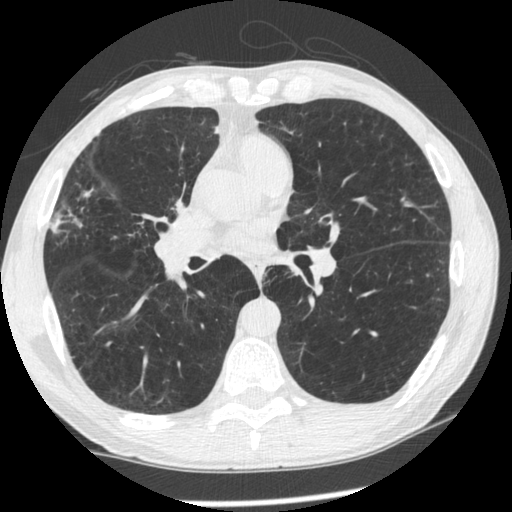
Low-dose screening chest CT, one axial slice. Slice 120 of 261 in the series (ordered by position). 120 kVp. Lung window (W 1500 / L -600 HU). 512 × 512 image matrix, field of view 340 × 340 mm.
Outlined on this slice (manually delineated by an expert):
- lesion 1 (tumor, upper lobe of right lung): bounding box <175,199,185,214> (left, top, right, bottom; pixels)